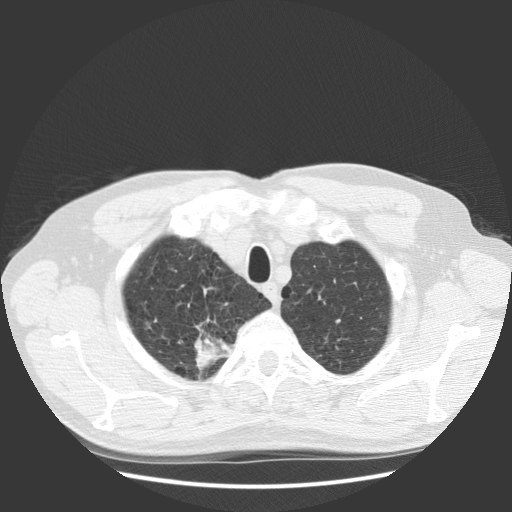
Low-dose screening chest CT, one axial slice; position 111 of 131 along the scan axis; reconstruction kernel STANDARD; 140 kVp; lung window (W 1500 / L -600 HU); 2.5 mm slice thickness; 512 × 512 image matrix, field of view 369 × 369 mm.
Outlined on this slice (expert manual segmentation):
- lesion 1 (tumor, upper lobe of right lung): box from (x=194, y=324) to (x=233, y=371) px